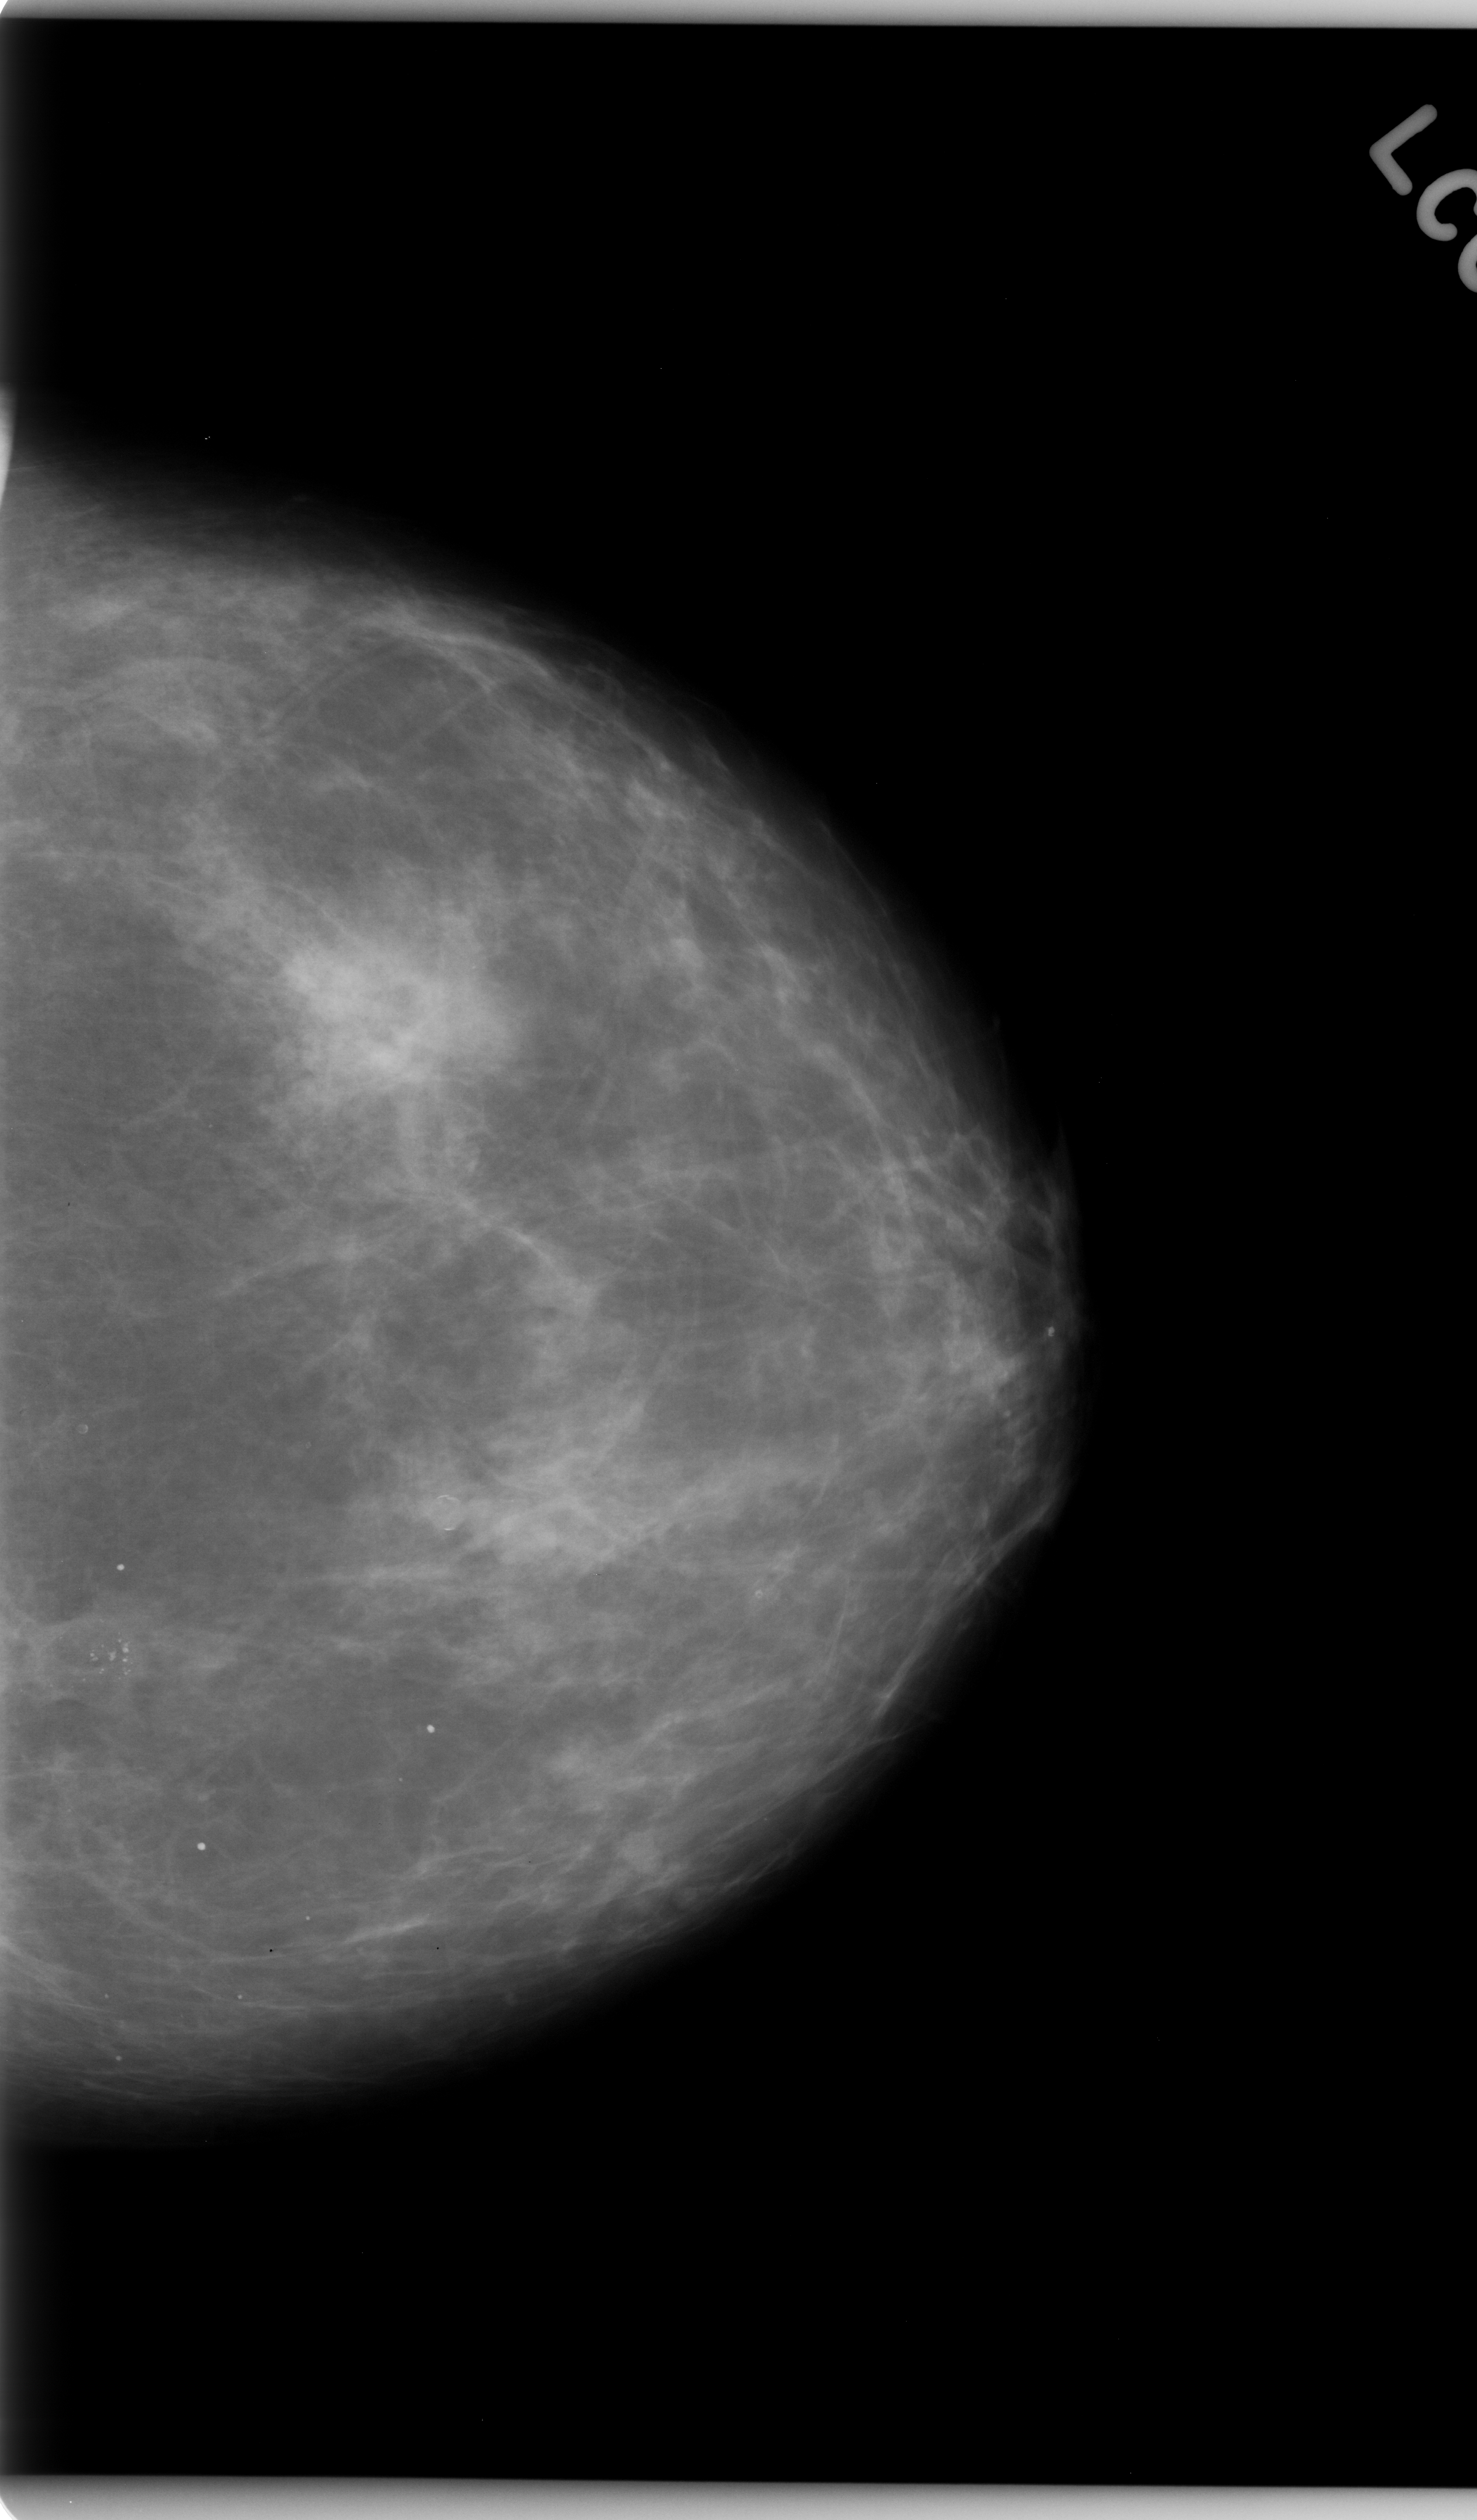
Scanned film-screen mammogram; left breast; CC view.
Radiologist-marked abnormalities on this image: calcifications, morphology amorphous, distribution clustered; BI-RADS assessment category 4; subtlety rating 5 on a 1 (subtle) to 5 (obvious) scale; pathology result (as recorded, not read from the image): benign.